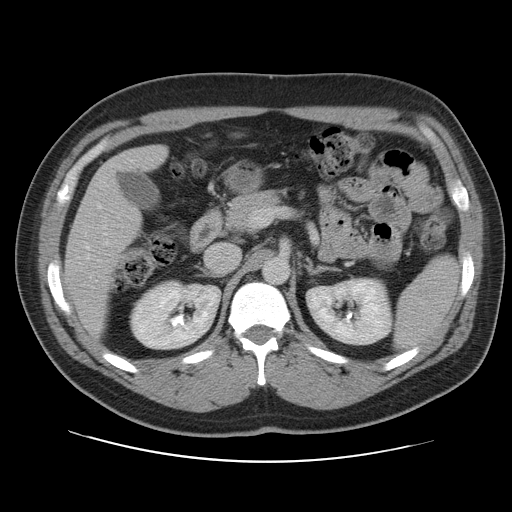
Contrast-enhanced abdominal CT, one axial slice; slice 60 of 109 in the series (ordered by position); 120 kVp; intravenous contrast given; soft-tissue window (W 400 / L 40 HU); 5 mm slice thickness; 512 × 512 image matrix, field of view 402 × 402 mm. Male patient, age 35 years. Case-level facts recorded for this patient, not image findings: diagnosis: colorectal cancer liver metastases, imaged before liver resection; multiple liver metastases: yes; largest metastasis: 2.8 cm; chemotherapy before resection: yes.
Outlined on this slice (expert manual segmentation):
- liver: bounding box [x1, y1, x2, y2] px = [66, 146, 201, 334]
- planned liver remnant (the part of the liver to remain after resection): [66, 146, 165, 334]